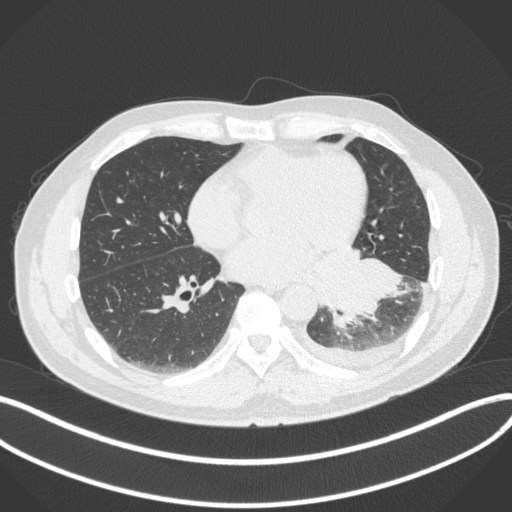
Chest CT, one axial slice. Slice 148 of 350 in the series (ordered by position). Reconstruction kernel B31f. Lung window (W 1500 / L -600 HU). 1 mm slice thickness. 512 × 512 image matrix, field of view 400 × 400 mm. Male patient, age 58 years. Case-level facts recorded for this patient, not image findings: clinical TNM (as recorded): T3 N1 M1b.
Structures marked on this image (rectangle marked by the reading radiologist):
- lung tumour (recorded histology: small cell carcinoma): bounding box (x1, y1, x2, y2) in pixels: (332, 253, 407, 334)